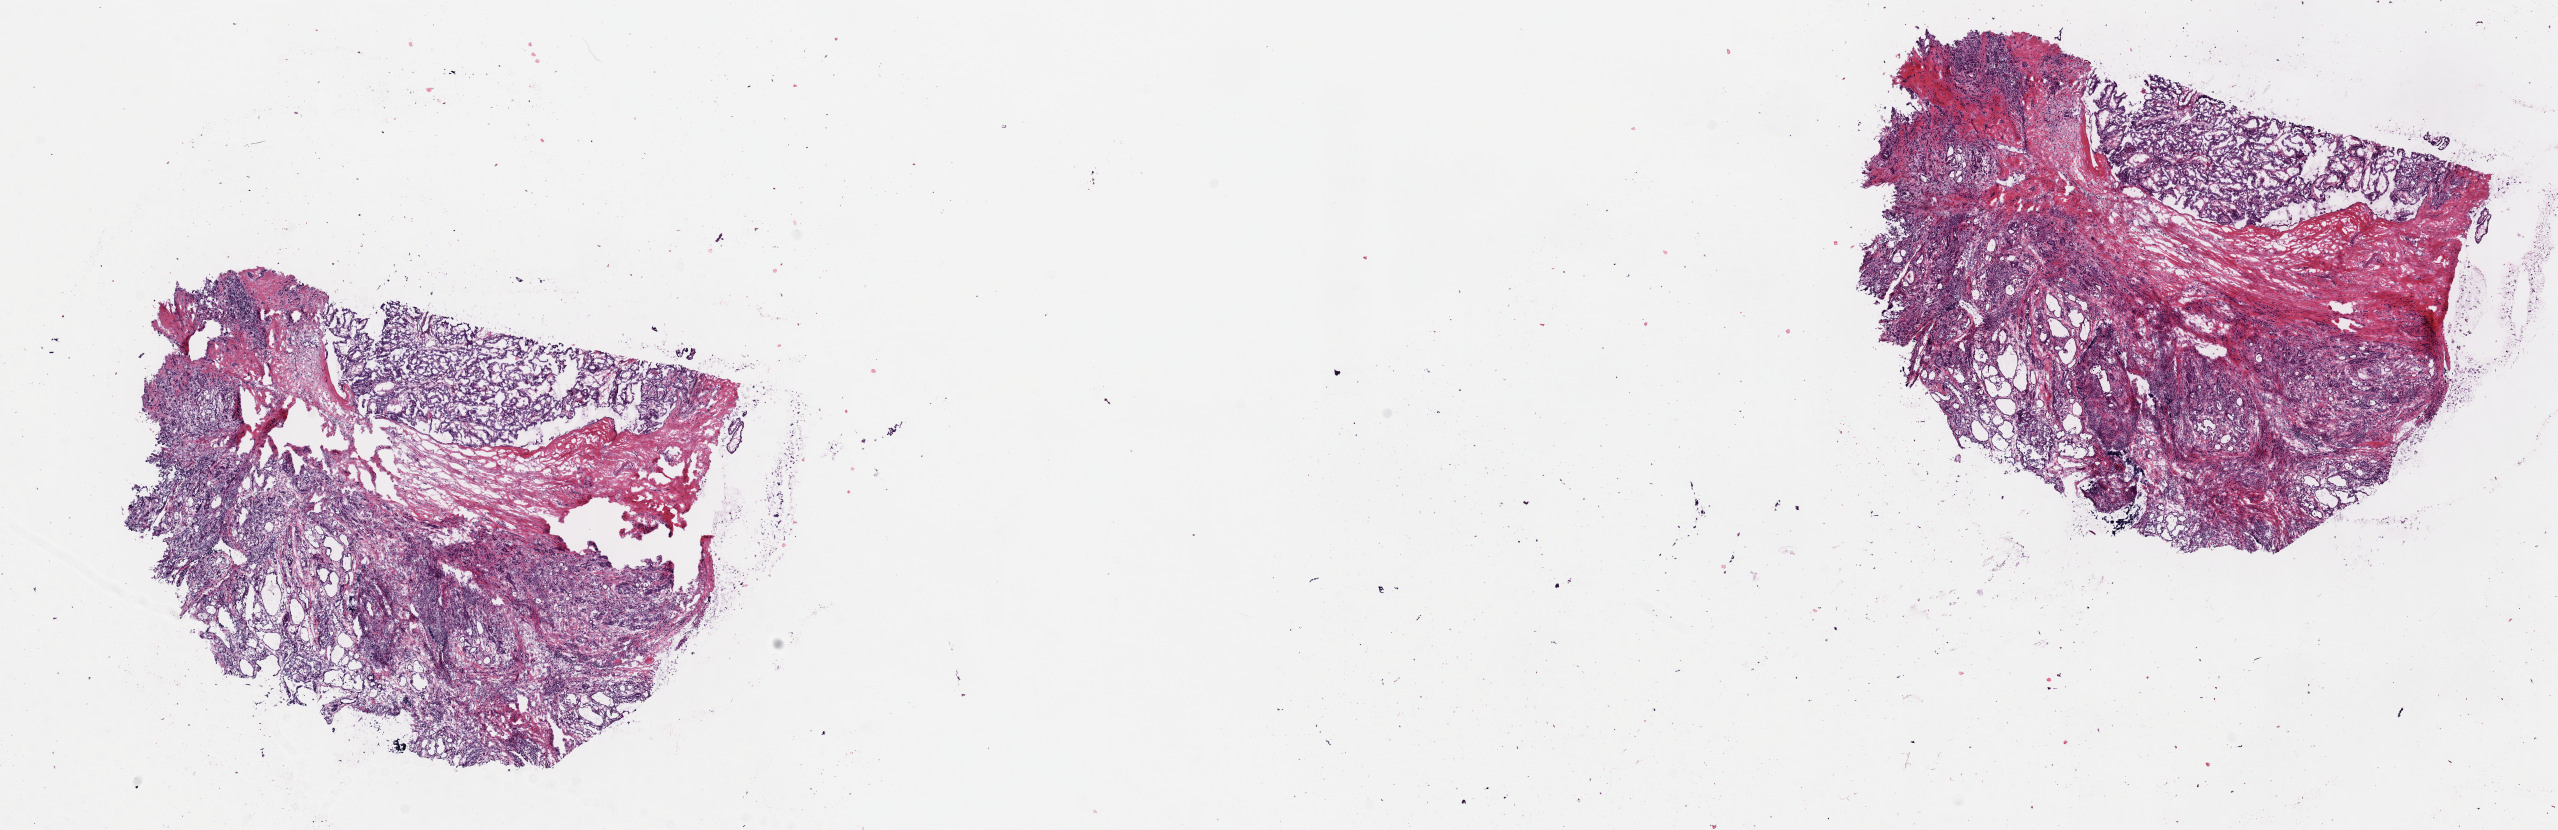
H&E-stained whole-slide image, low-resolution overview of the scanned area, about 20.2 x 6.6 mm. Frozen section. Thyroid, primary tumour sample. Patient: female, age at initial diagnosis 34 years. Slide review estimates, as recorded: tumour cells 60%, tumour nuclei 60%, normal cells 10%, stromal cells 30%, necrosis 0%. Inflammatory infiltration, as recorded: lymphocyte infiltration 10%, monocyte infiltration 0%, neutrophil infiltration 0%.
* lymph nodes positive (case pathology): 3 of 9 examined
* histologic diagnosis: Papillary adenocarcinoma, NOS (thyroid gland)
* TNM: T1 N1a M0
* AJCC pathologic stage: I (7th edition)